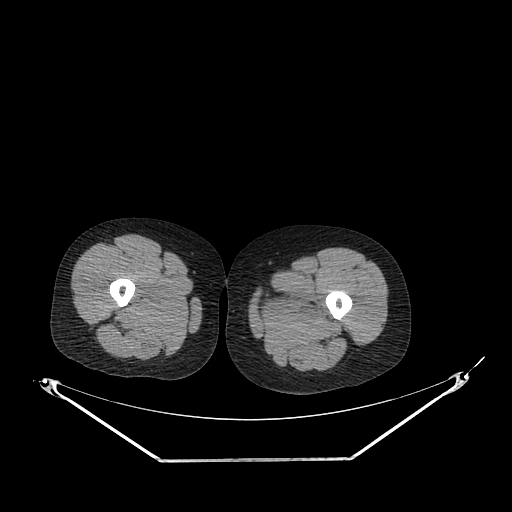
CT of an extremity soft-tissue mass (from a PET/CT study), one axial slice; slice 224 of 267 in the series (ordered by position); reconstruction kernel SOFT; soft-tissue window (W 400 / L 40 HU); 3.75 mm slice thickness; 512 × 512 image matrix, field of view 500 × 500 mm. Female patient. From the clinical record (not read from this slice): histological type: pleiomorphic leiomyosarcoma; grade: intermediate; site of the primary tumour: left thigh.
Outlined on this slice (expert contour drawn on MRI and transferred to this co-registered scan by the dataset authors):
- gross tumour volume including surrounding oedema: bounding box (x1, y1, x2, y2) in pixels: (260, 285, 323, 318)